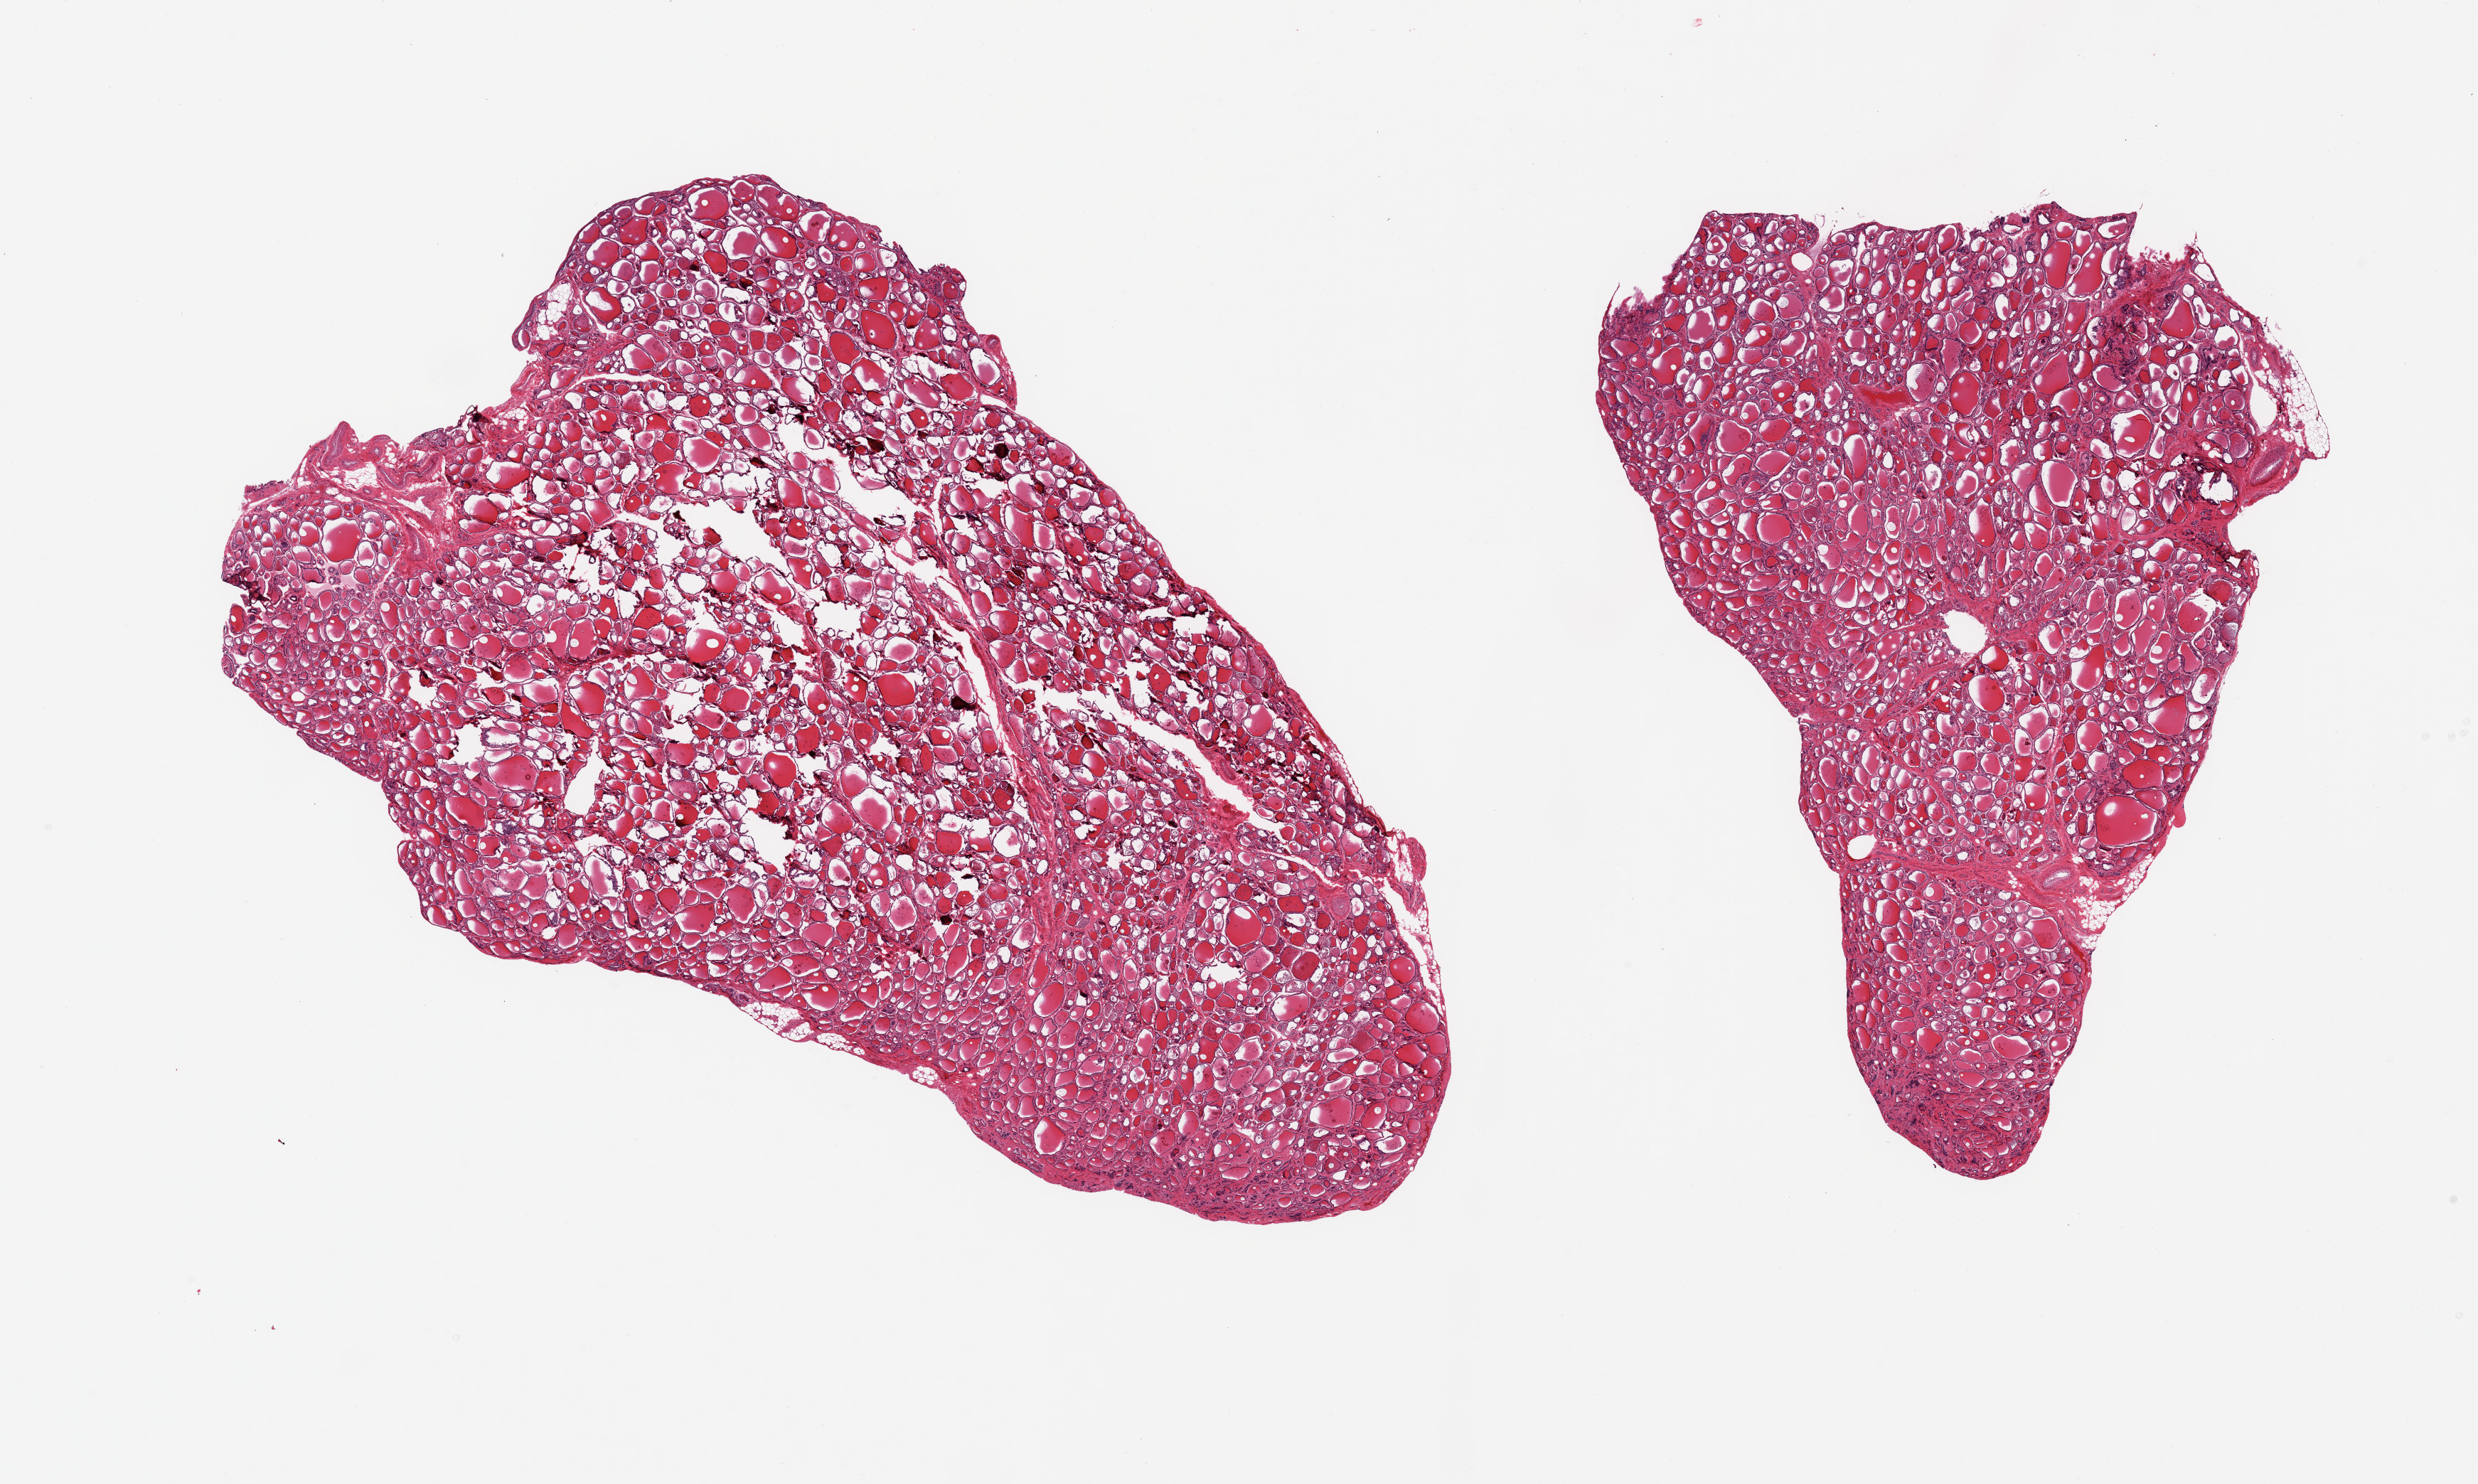
Hematoxylin and eosin (H&E) whole-slide image, low-resolution overview of the scanned area, about 27.6 x 16.5 mm, PAXgene-fixed paraffin-embedded (PFPE) section, section of thyroid (target tissue), donor tissue sample. Donor sex: male.
- pathologist's review note for this sample: 2 pieces, no abnromalities